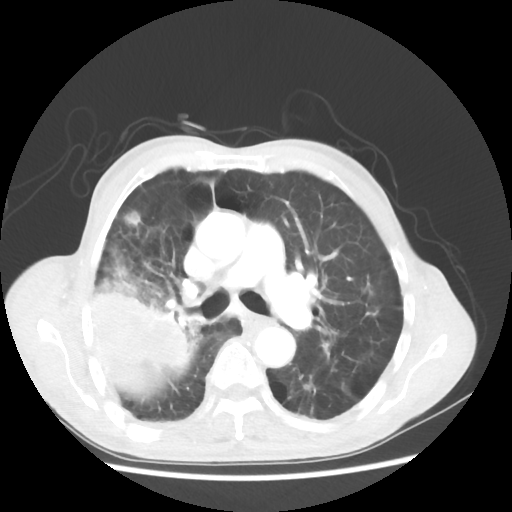
Chest CT, one axial slice. Slice 33 of 58 in the series (ordered by position). 100 kVp. Lung window (W 1500 / L -600 HU). 5 mm slice thickness. 512 × 512 image matrix, field of view 351 × 351 mm. Patient: male, 75 years. From the clinical record (not read from this slice): clinical TNM (as recorded): T4 N1 M1.
Annotated regions visible in this slice (rectangle marked by the reading radiologist):
- lung tumour (recorded histology: adenocarcinoma): bounding box <85,266,203,404> (left, top, right, bottom; pixels)